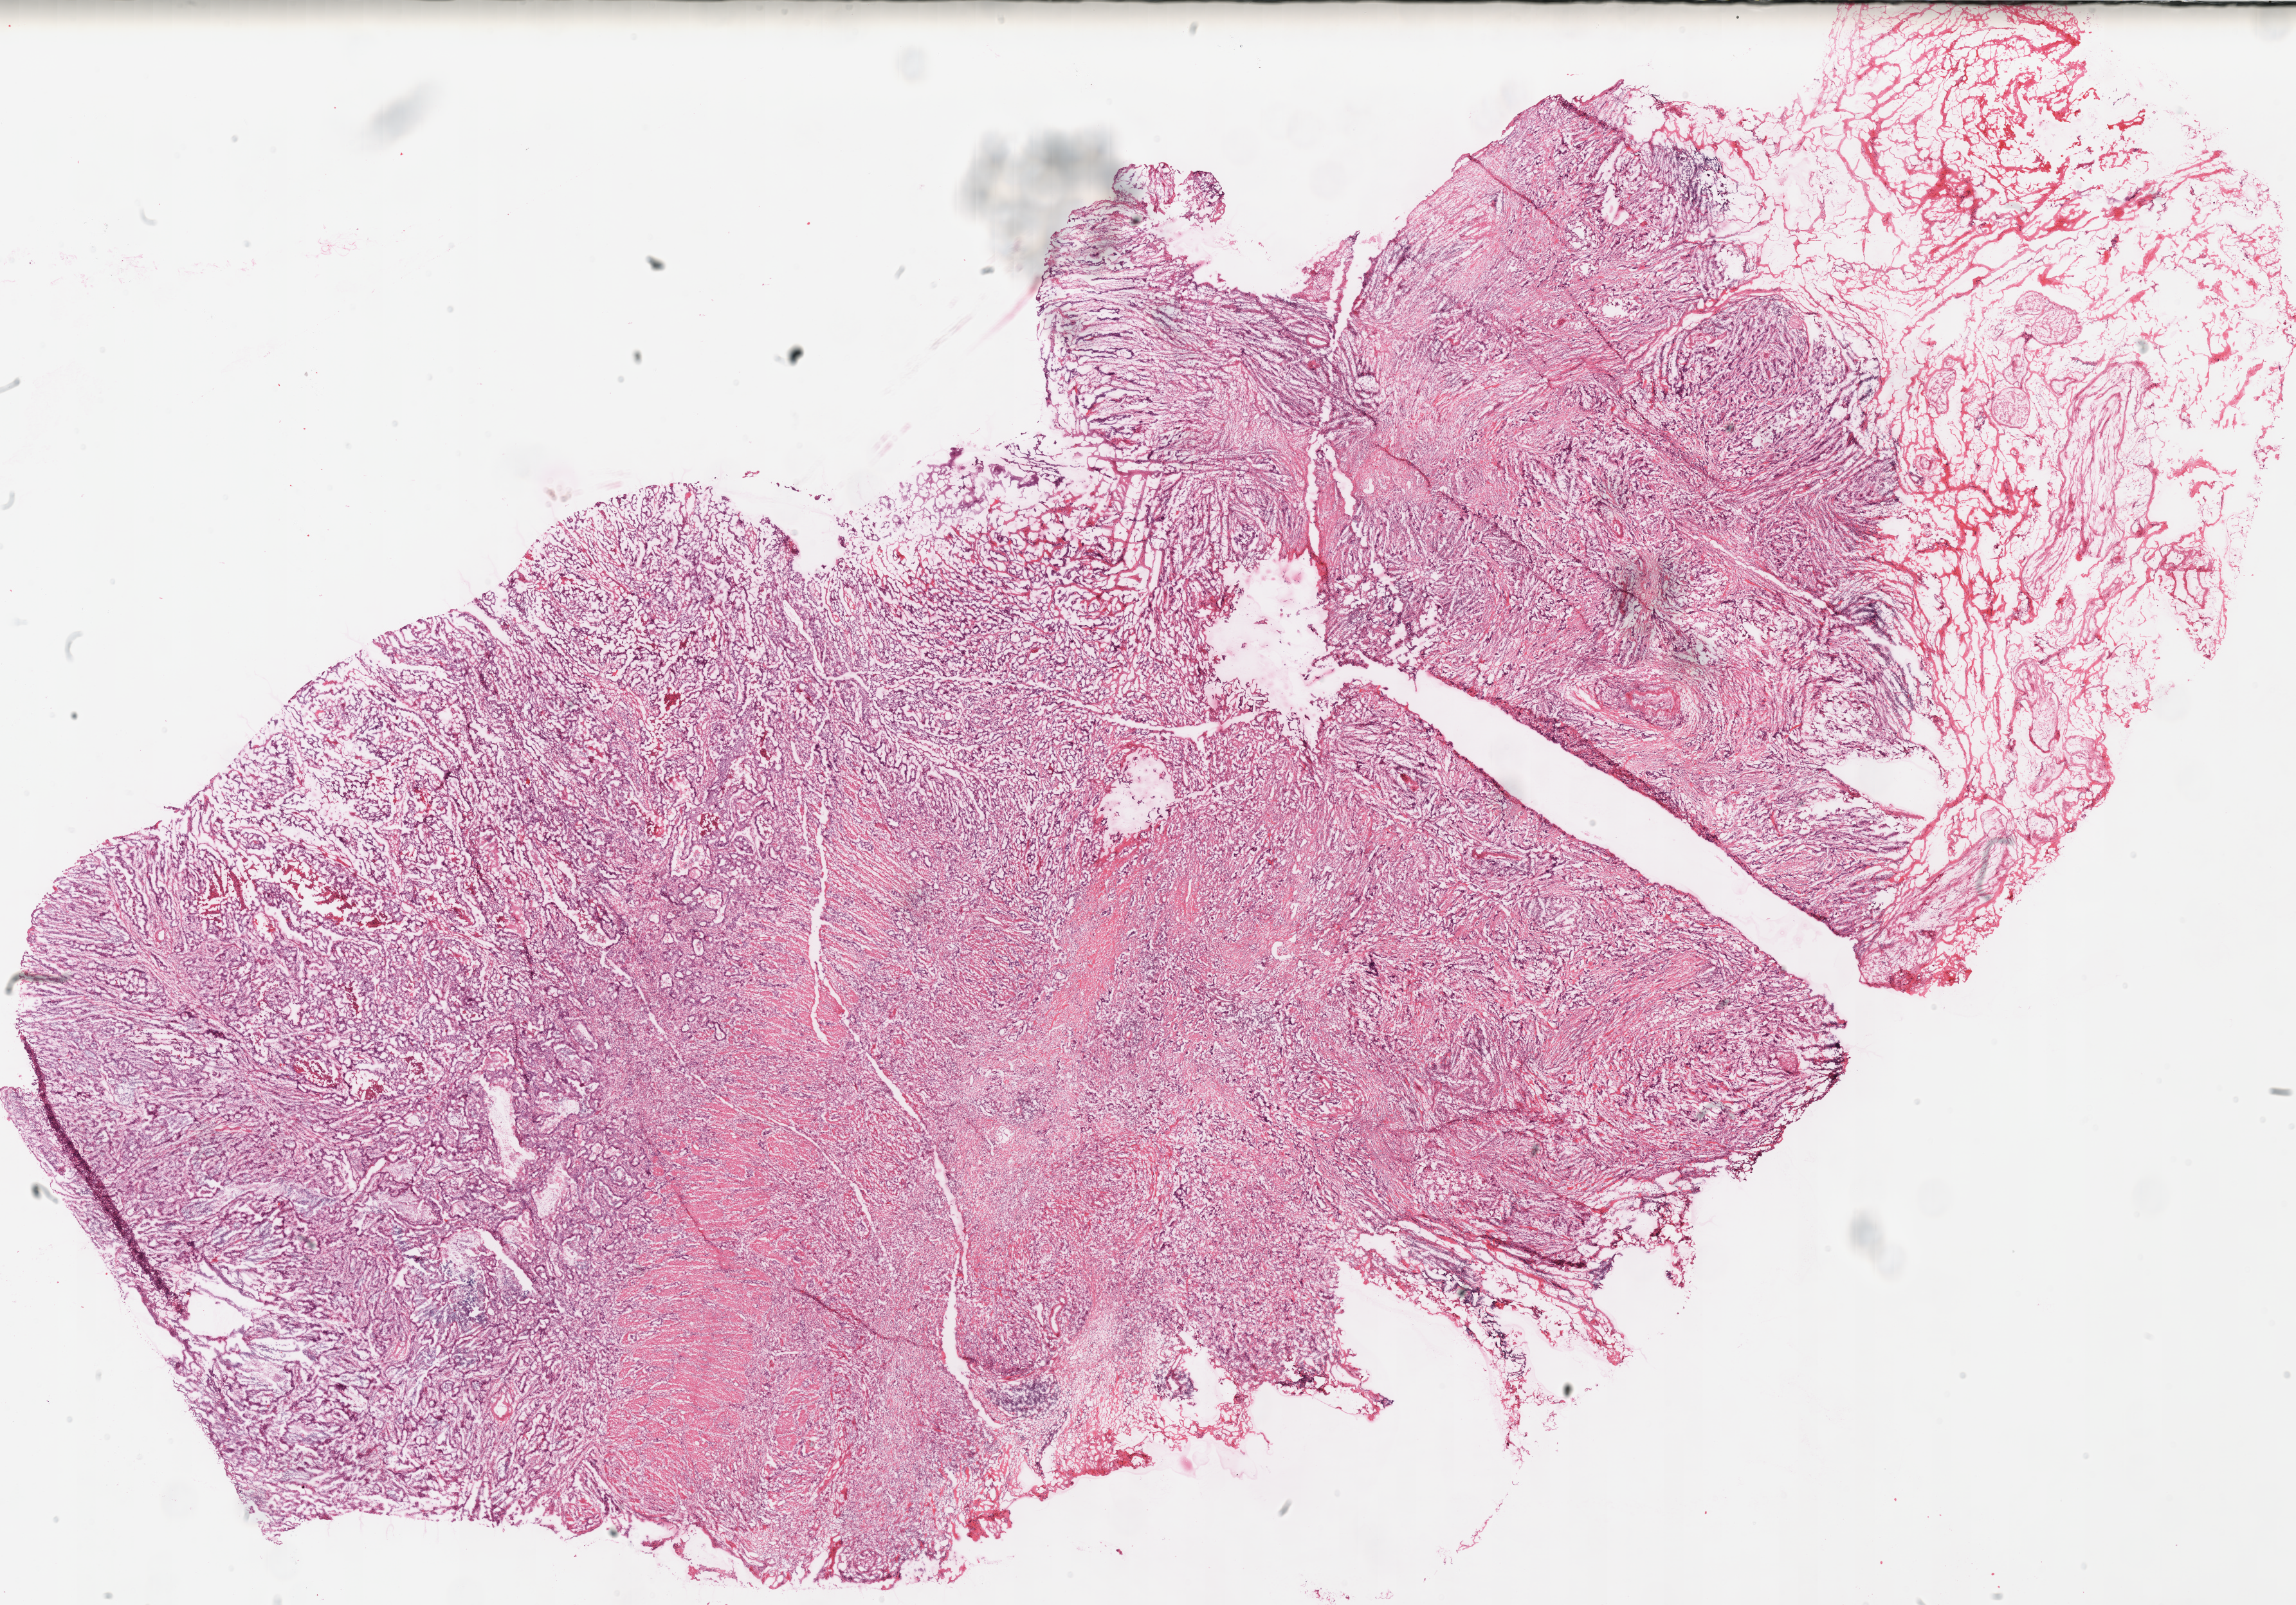
Whole-slide histology image, Hematoxylin and eosin (H&E) stained, low-resolution overview of the scanned area, about 28.1 x 19.7 mm (acquisition: 40x scan), frozen section from the top of the tissue portion, stomach, primary tumour sample. Patient: female, age at initial diagnosis 54 years. Histologic grade: G2 (moderately differentiated). Pathologist review of this section (percent, as recorded): tumour cells 85%, tumour nuclei 65%, normal cells 0%, stromal cells 10%, necrosis 5%. Infiltration values recorded for this section: lymphocyte infiltration 10%, monocyte infiltration 5%, neutrophil infiltration 10%.
* lymph nodes positive (case pathology): 10 of 10 examined
* histologic diagnosis: Adenocarcinoma, NOS
* AJCC pathologic stage: IIIB (7th edition)